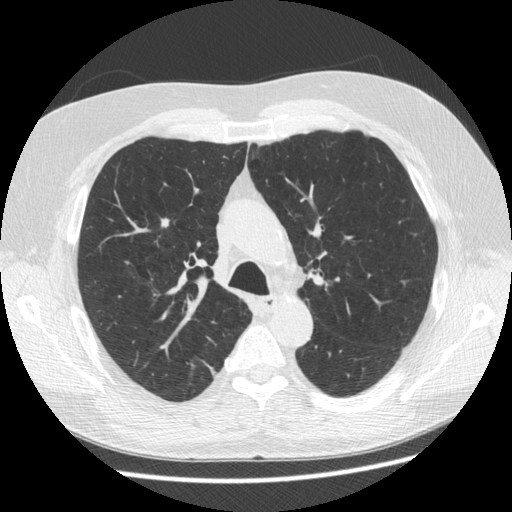
Chest CT (low-dose screening protocol), one axial image. Third annual screen. Lung window (W 1500 / L -600 HU). Slice 164 of 545 in the series. Male participant, aged 63 years at enrolment.
Expert-annotated lung lesion, bounding box (x1, y1, x2, y2) in pixels: (150, 209, 182, 238). The screening reader recorded 2 non-calcified nodules or masses ≥4 mm on this exam; which of them this box marks is not recorded.